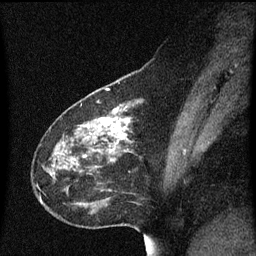
Breast MRI (dynamic contrast-enhanced), one sagittal slice; slice 22 of 60 in the series (ordered by position); dynamic contrast-enhanced series, image 2 of 3 at this slice position (ordered by acquisition); 1.5 T; TE 4.2 ms, TR 8.4 ms; 256 × 256 image matrix, field of view 200 × 200 mm. Patient: female, 49 years. From the clinical record (not read from this slice): setting: breast cancer imaged before/during neoadjuvant chemotherapy; receptor status: HR-positive, HER2-negative.
Structures marked on this image (semi-automatic segmentation, software-assisted and operator-edited):
- analysis volume of interest (the breast-tissue region the enhancement analysis was run in; not a lesion): bounding box <33,96,174,215> (left, top, right, bottom; pixels)
- tumour enhancement mask (voxels above the 70 % enhancement threshold inside the analysis volume of interest): <99,118,129,139>